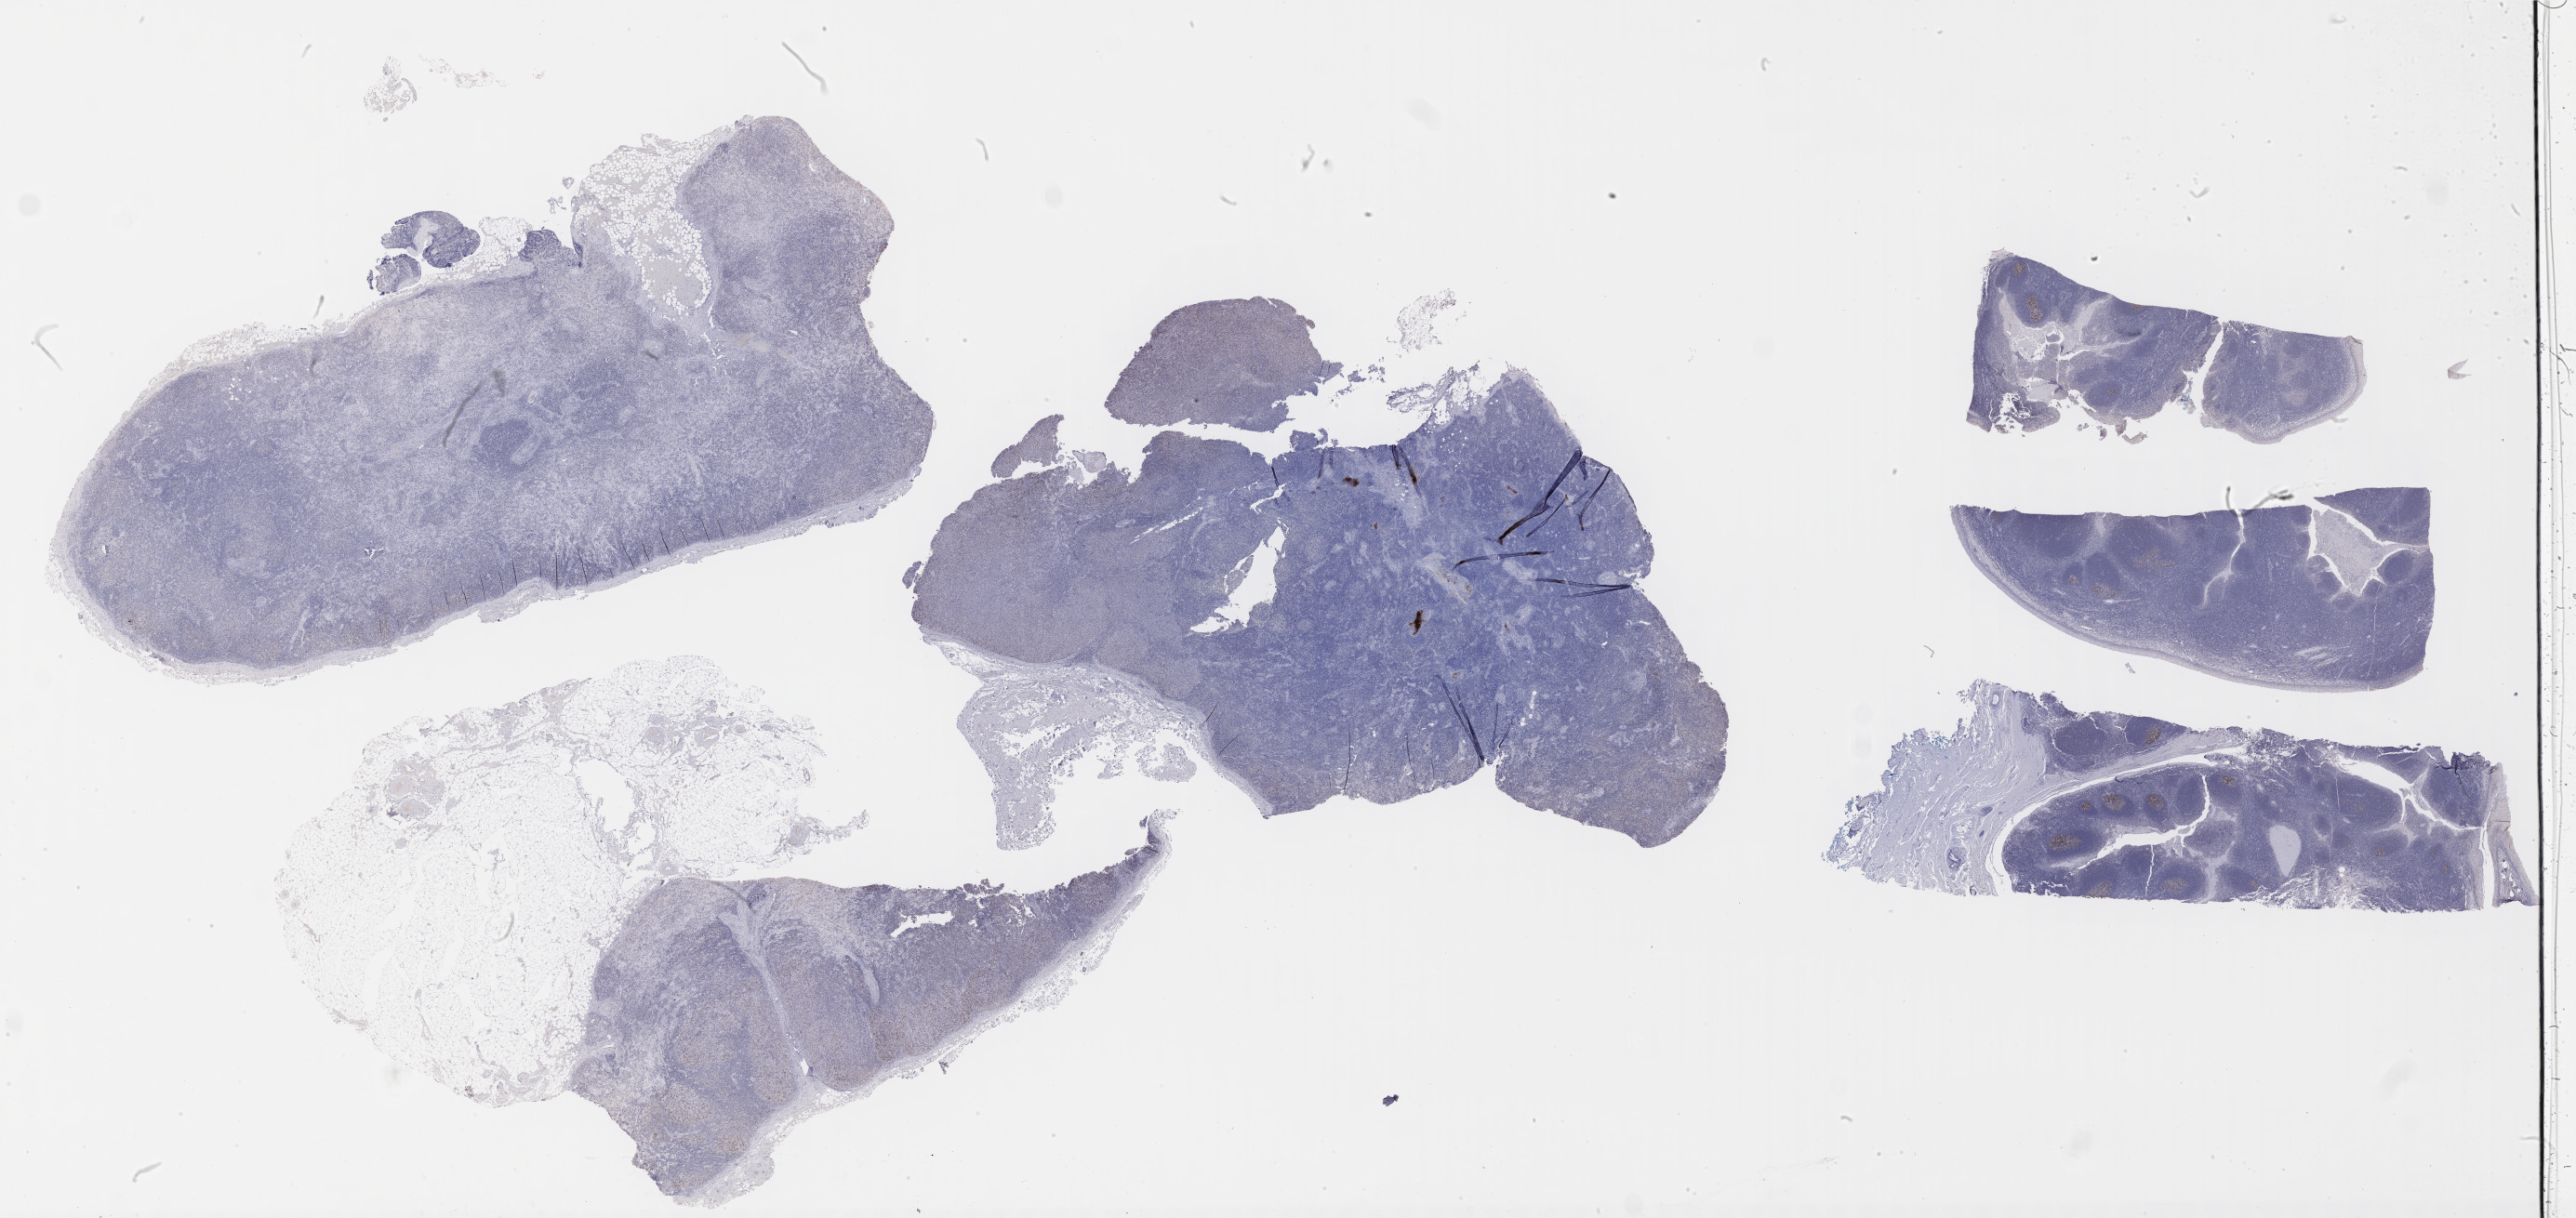
IHC for BCL6, whole-slide image — shown as a low-resolution overview of the whole scanned area (about 44.8 x 21.2 mm); specimen: tumor tissue; site: lymph node. Patient: male, aged 56.
Histologic diagnosis: Diffuse large B-cell lymphoma, NOS.